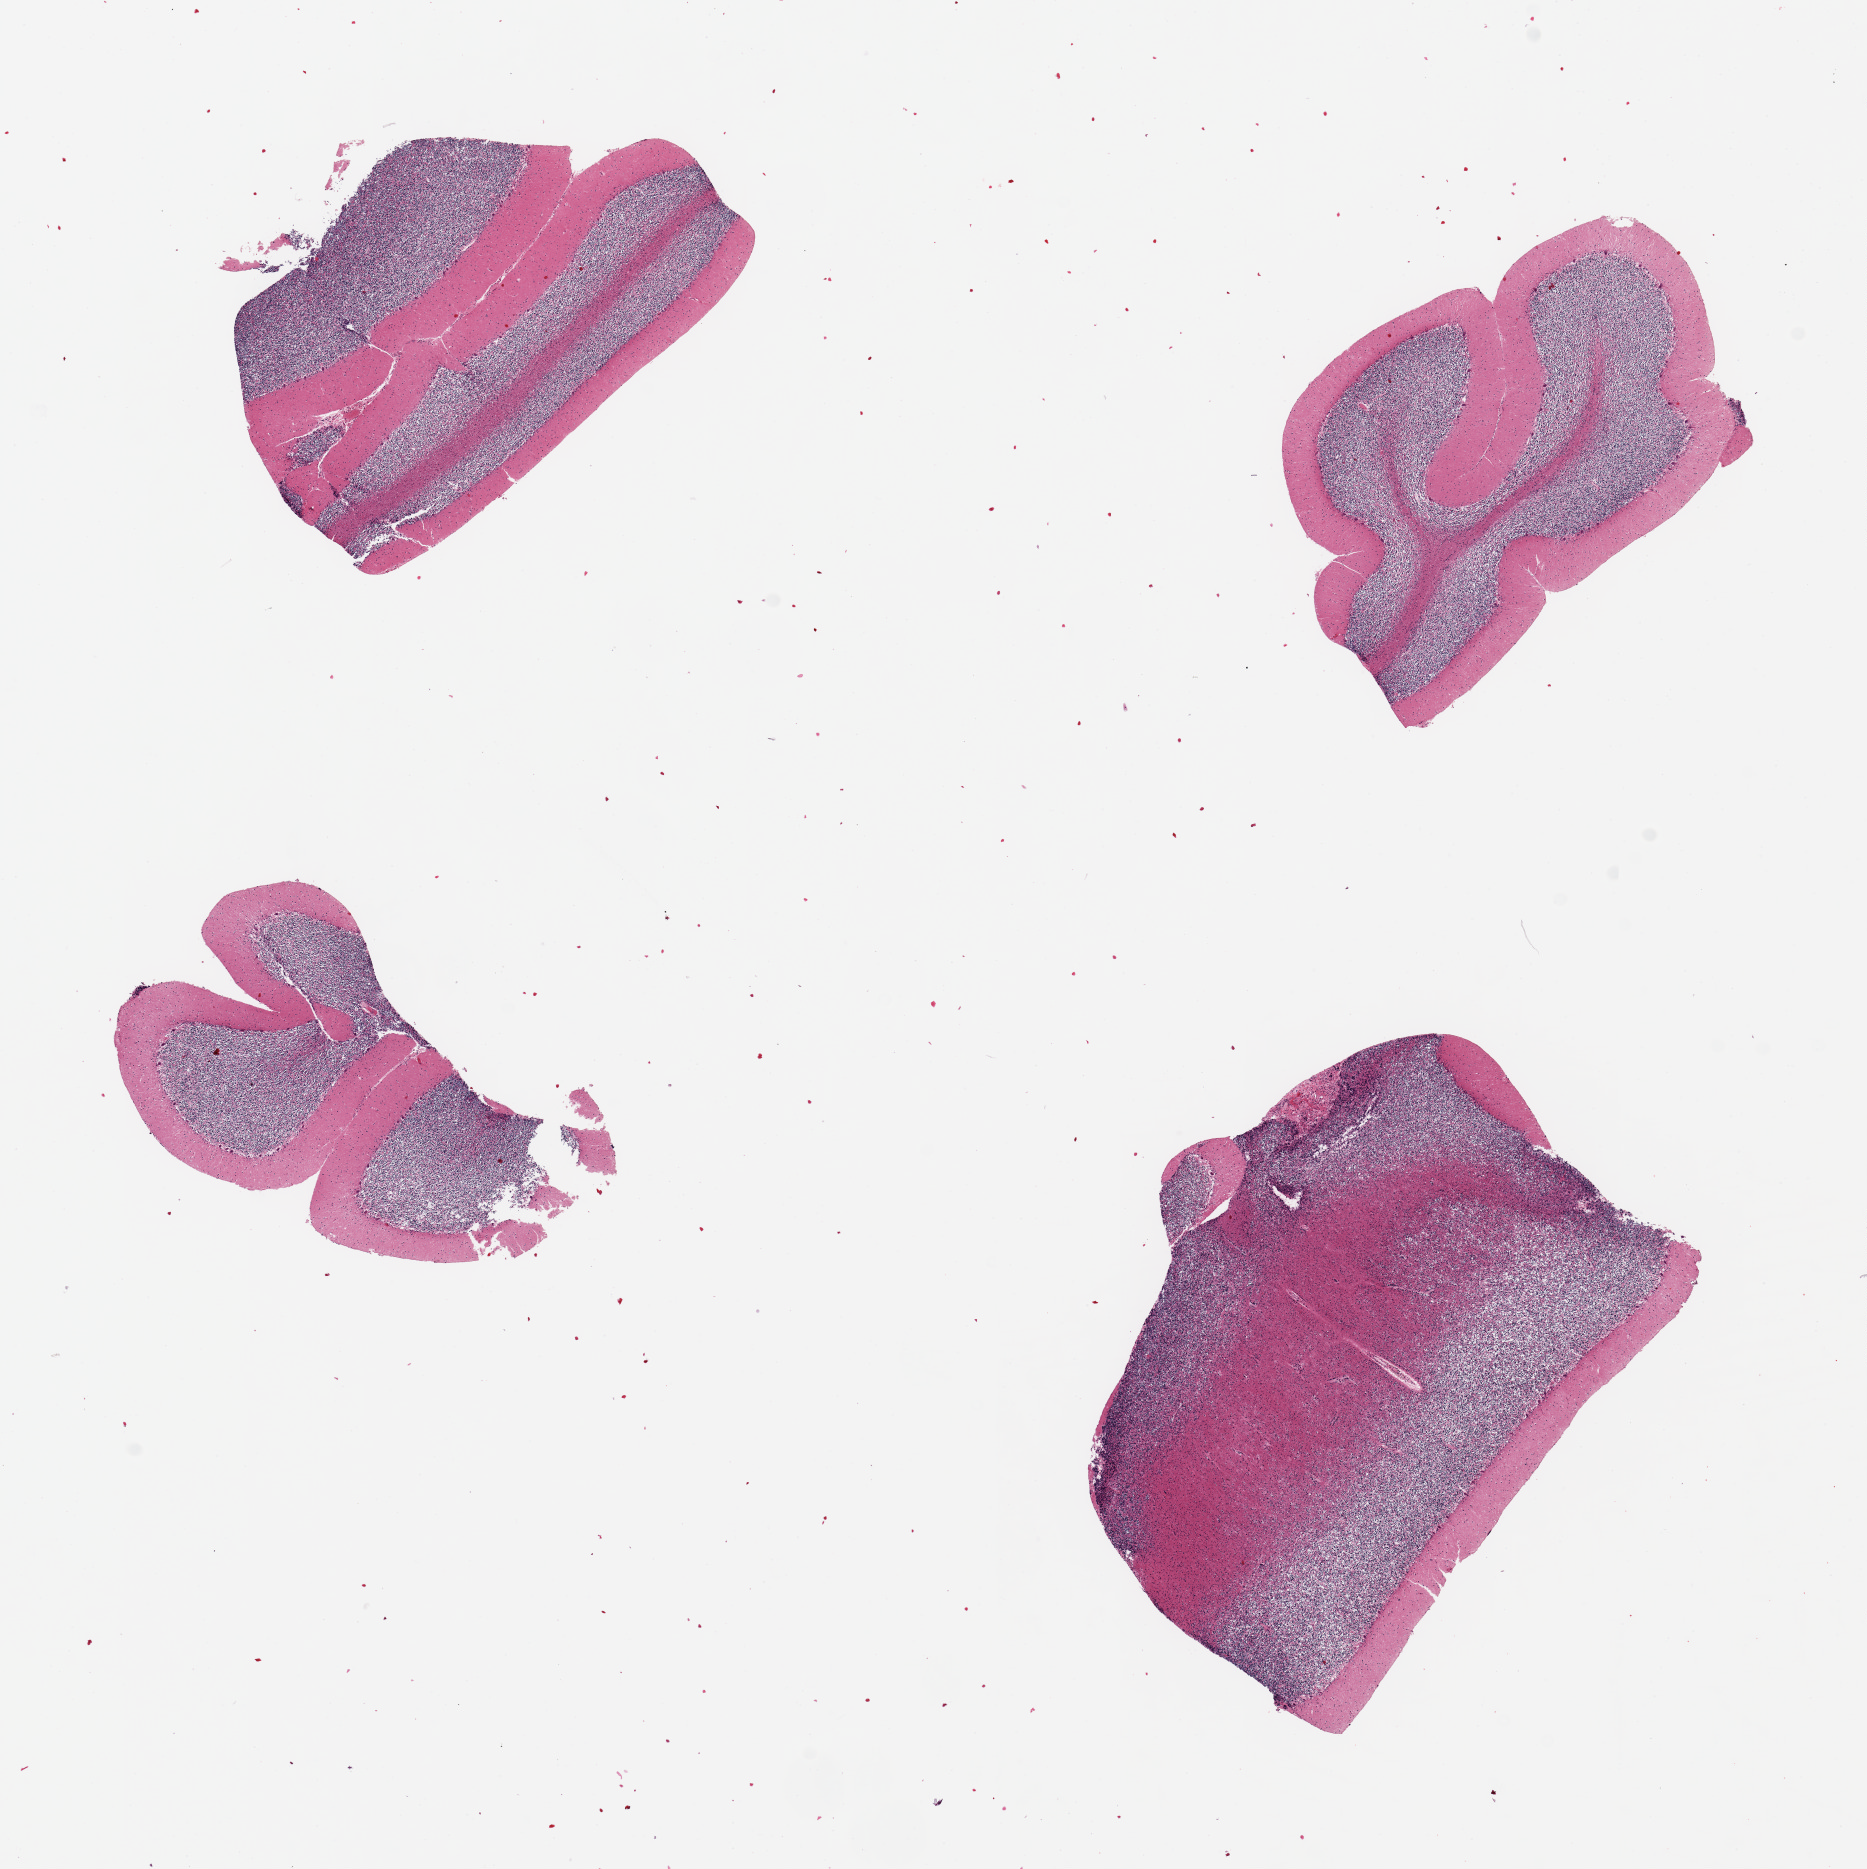
Whole-slide image, H&E stain, whole scanned area (about 14.8 x 14.8 mm) shown as a low-resolution overview. PAXgene-fixed, paraffin-embedded tissue. Sampled site (target tissue): cerebellum. Tissue donor sample. Female donor.
Reviewer comment on this tissue sample: 4 pieces, up to 5x3mm; Purkinje cells well defined.